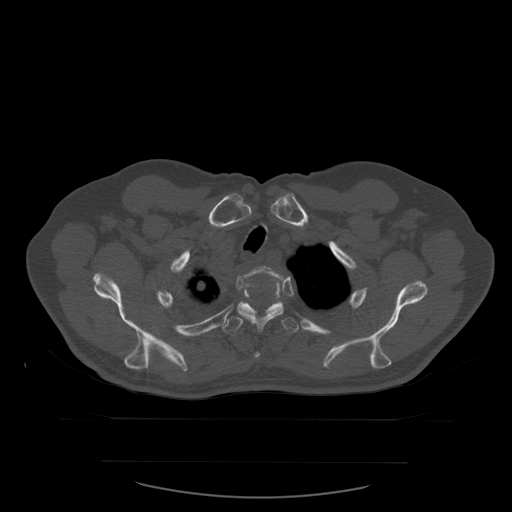
CT including the spine, one axial slice; slice 455 of 590 in the series (ordered by position); bone window (W 1800 / L 400 HU); 1.25 mm slice thickness; 512 × 512 image matrix, field of view 479 × 479 mm. Patient age 71 years. From the clinical record (not read from this slice): primary cancer: lung; vertebrae with lytic lesions (as recorded): T1, T2, L5, S1.
Annotated regions visible in this slice (semi-automatic segmentation, software-assisted and operator-edited):
- T2 vertebra: bounding box [x1, y1, x2, y2] px = [246, 266, 283, 281]
- T3 vertebra: [237, 277, 284, 358]
- T4 vertebra: [222, 296, 299, 335]